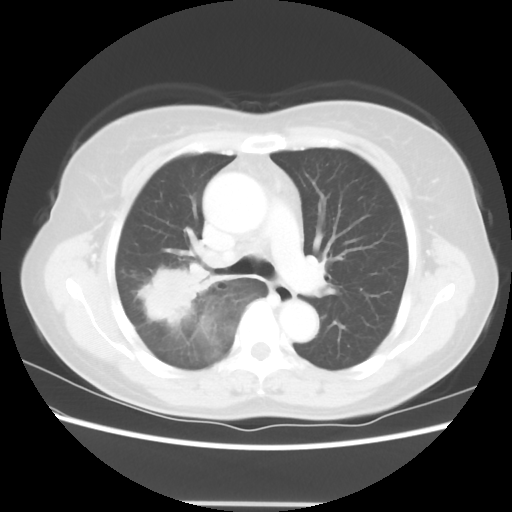
Chest CT, one axial slice. Slice 38 of 56 in the series (ordered by position). Reconstruction kernel STANDARD. 120 kVp. Lung window (W 1500 / L -600 HU). 5 mm slice thickness. 512 × 512 image matrix, field of view 360 × 360 mm. Patient: female, 55 years. Case-level facts recorded for this patient, not image findings: clinical TNM (as recorded): T2 N1 M0; histopathological grade: G2-3.
Annotated regions visible in this slice (bounding box drawn by a radiologist):
- lung tumour (recorded histology: adenocarcinoma): bounding box [x1, y1, x2, y2] px = [131, 250, 202, 334]